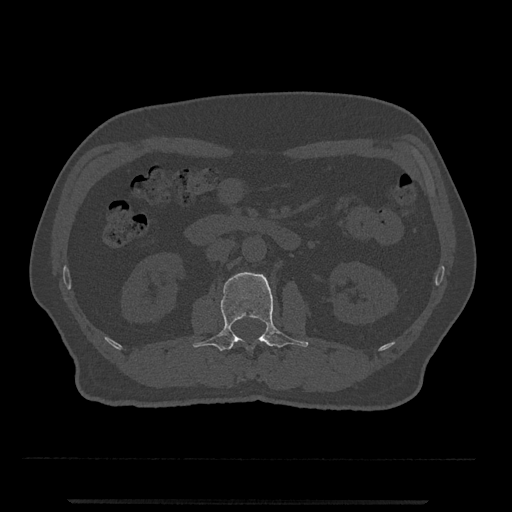
CT including the spine, one axial slice. Slice 275 of 797 in the series (ordered by position). Reconstruction kernel Br40s/3. 120 kVp. Bone window (W 1800 / L 400 HU). 512 × 512 image matrix. Patient: male, 63 years. Case-level facts recorded for this patient, not image findings: primary cancer: prostate.
Annotated regions visible in this slice (semi-automatic segmentation, software-assisted and operator-edited):
- L2 vertebra: bounding box <193,272,309,351> (left, top, right, bottom; pixels)